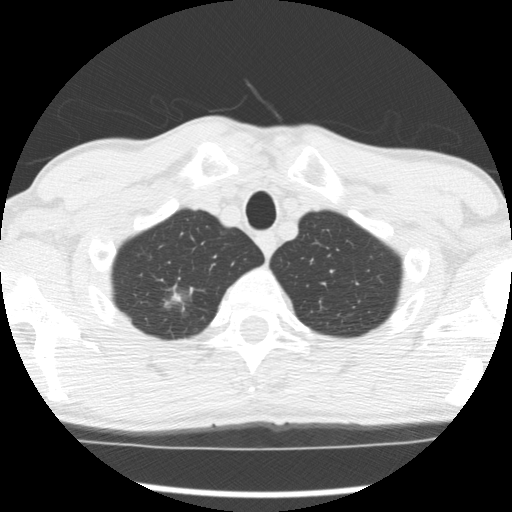
Low-dose screening chest CT, axial slice; first (baseline) screen; lung window (W 1500 / L -600 HU); standard (soft-tissue) reconstruction kernel (STANDARD); slice 28 of 277 in the series. Male, age 66 years at enrolment.
Expert reader's lesion annotation, bounding box [x1, y1, x2, y2] px = [156, 282, 201, 326]. The screening reader recorded 4 non-calcified nodules or masses ≥4 mm on this exam (right upper lobe, right upper lobe, right upper lobe, left lower lobe); which of them this box marks is not recorded. Official screen result: positive, change unspecified: nodule(s) >= 4 mm or enlarging nodule(s), mass(es), or other non-specific abnormalities suspicious for lung cancer. Lung cancer was diagnosed 503 days after this screen (after the second annual screen): adenocarcinoma, NOS, right upper lobe, undifferentiated (G4), stage IA (AJCC 6th edition), 20 mm at pathology.